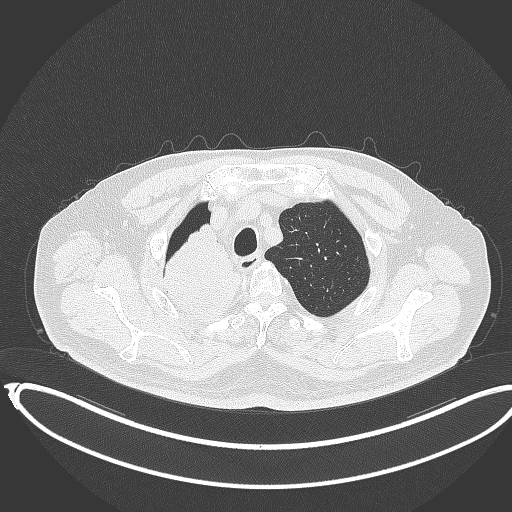
Chest CT, one axial slice. Position 313 of 403 along the scan axis. 120 kVp. Lung window (W 1500 / L -600 HU). 512 × 512 image matrix, field of view 436 × 436 mm. Male patient, age 68 years. Case-level facts recorded for this patient, not image findings: clinical TNM (as recorded): T2a N0 M0.
Structures marked on this image (bounding box drawn by a radiologist):
- lung tumour (recorded histology: adenocarcinoma): bounding box [x1, y1, x2, y2] px = [157, 223, 246, 319]